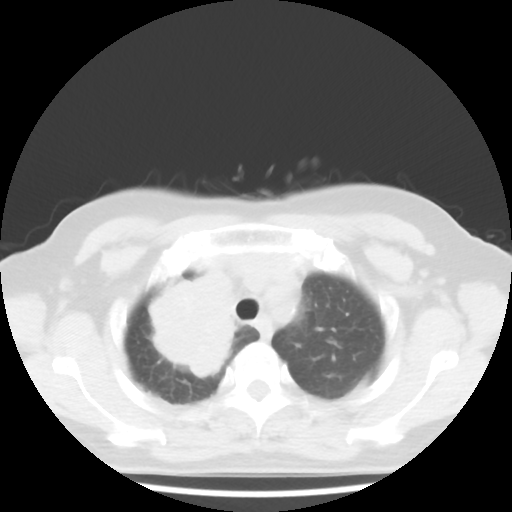
Chest CT, one axial slice. Position 35 of 43 along the scan axis. Lung window (W 1500 / L -600 HU). 5 mm slice thickness. 512 × 512 image matrix. Patient: female, 62 years. Case-level facts recorded for this patient, not image findings: clinical TNM (as recorded): T3 N0 M0; histopathological grade: G3.
Structures marked on this image (bounding box drawn by a radiologist):
- lung tumour (recorded histology: small cell carcinoma): box from (x=134, y=268) to (x=251, y=395) px